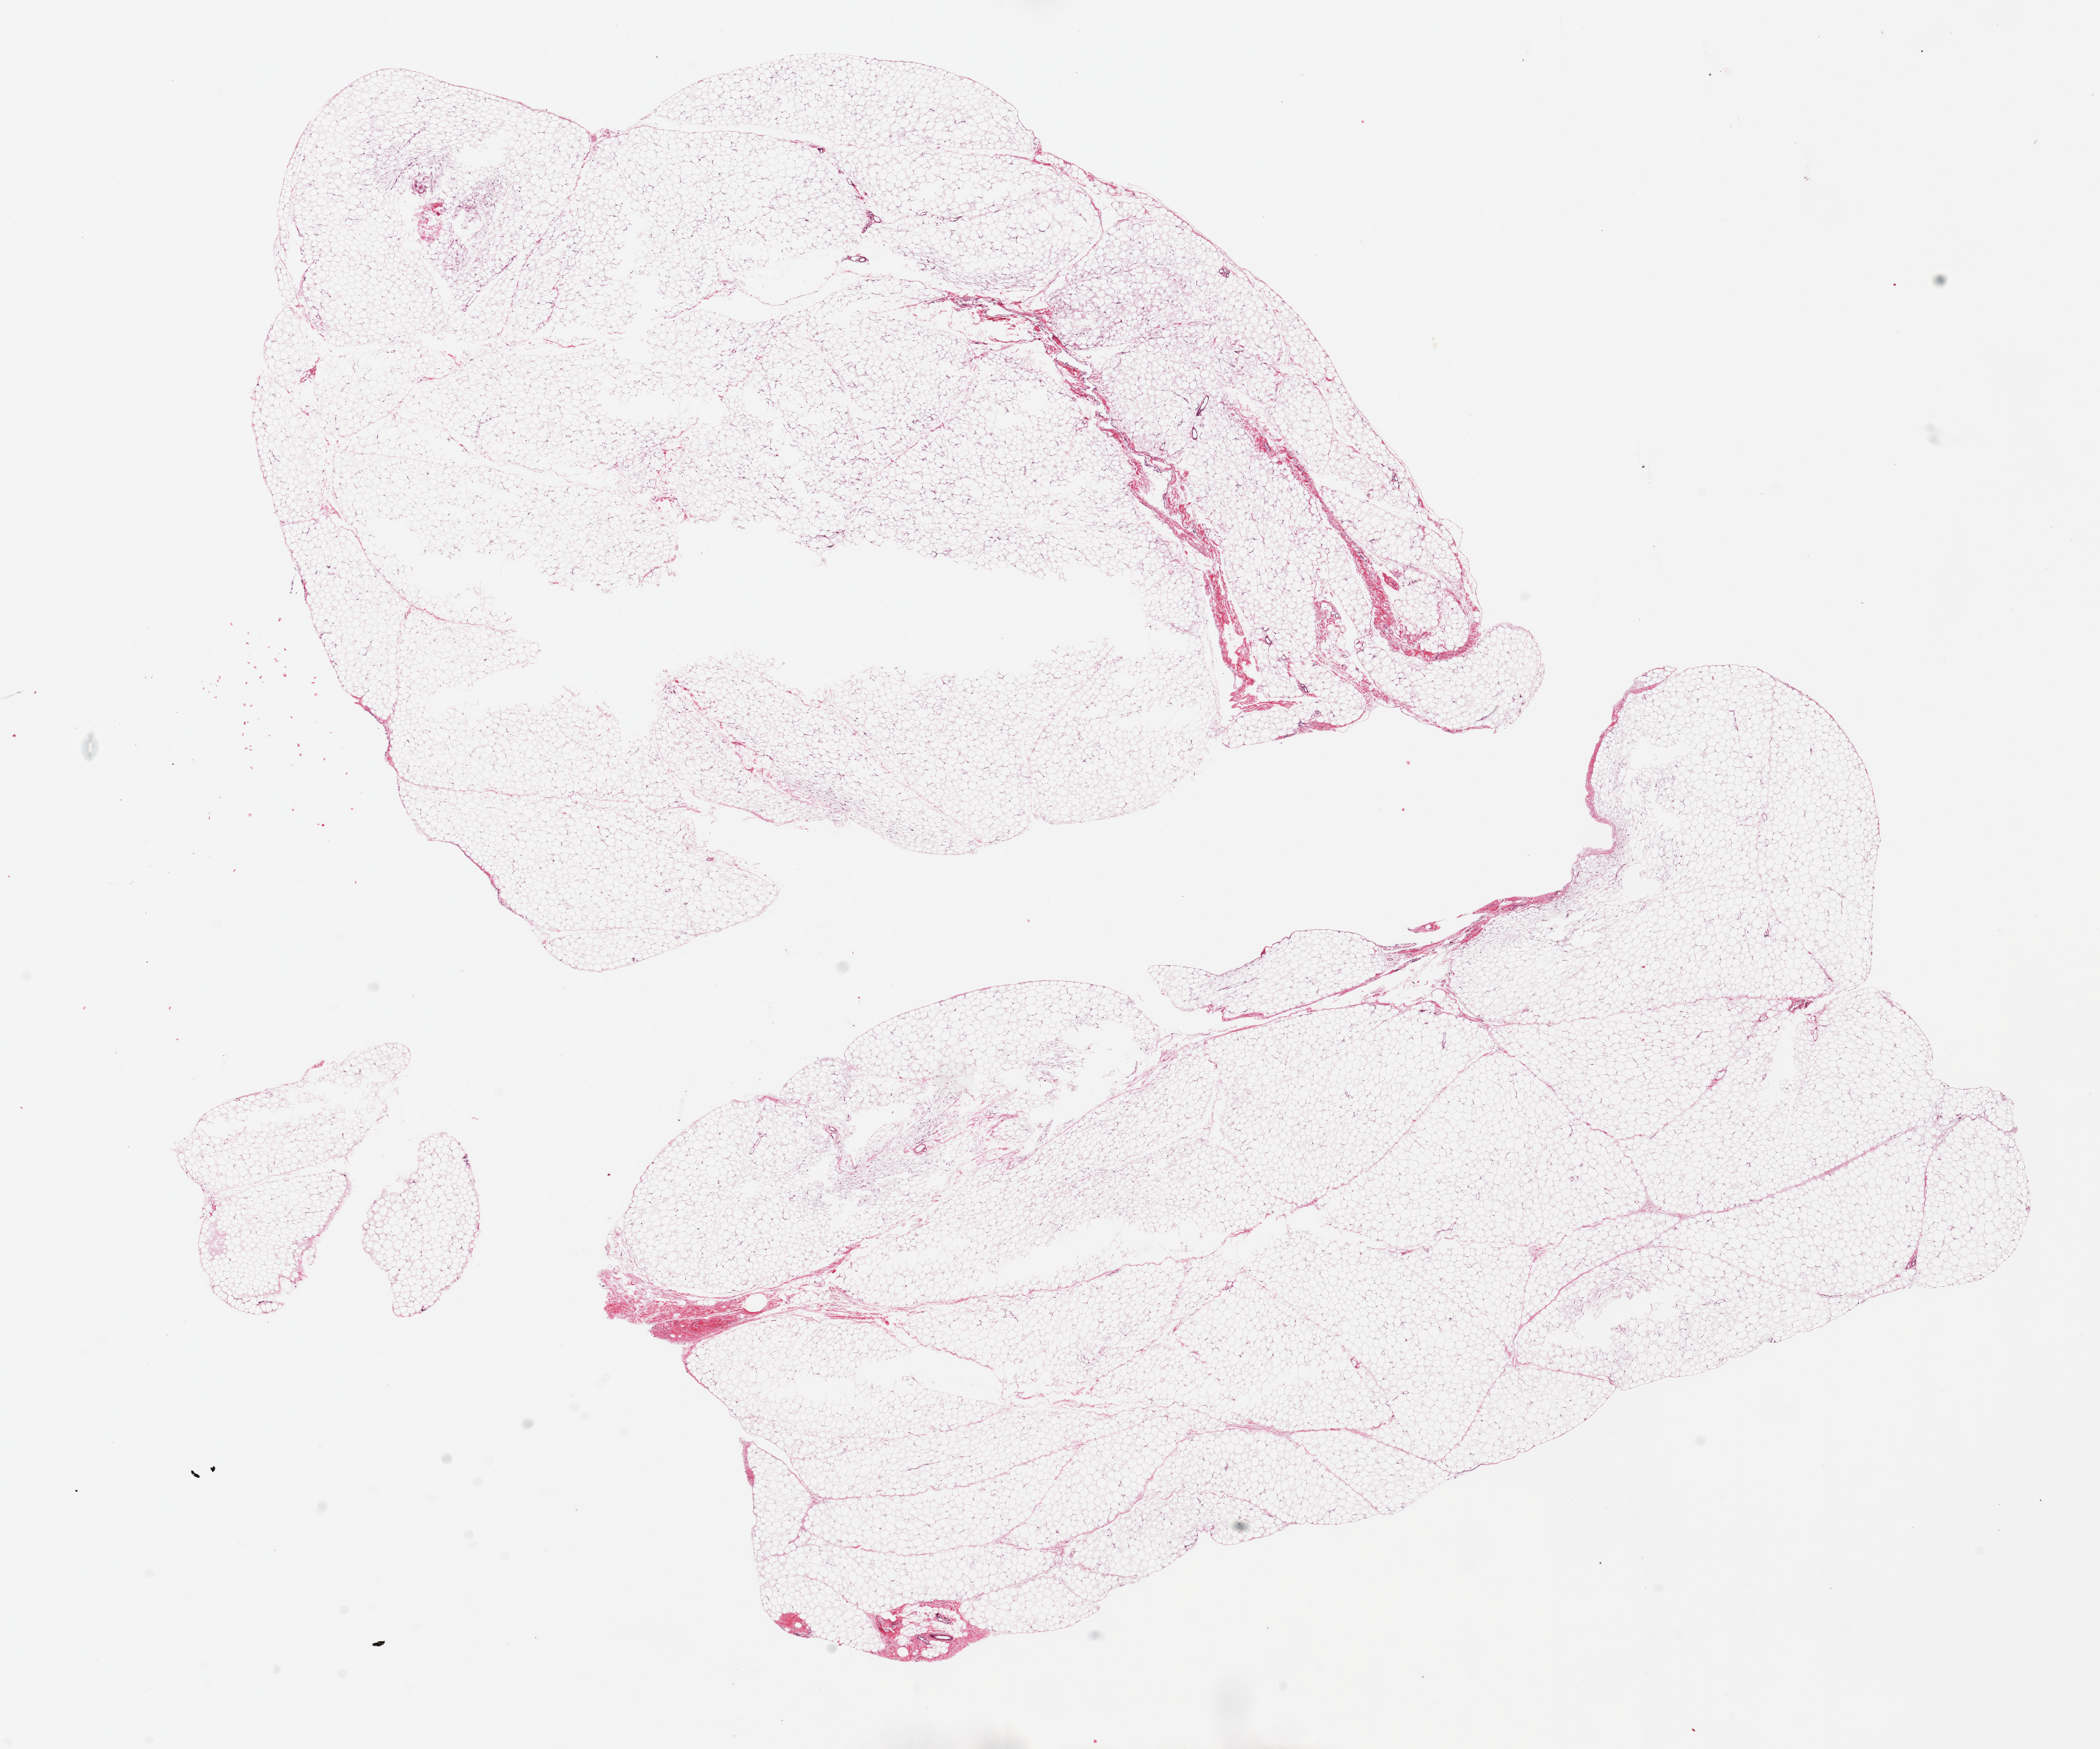
Hematoxylin and eosin (H&E) whole-slide image, brightfield — shown as a low-resolution overview of the whole scanned area (about 22.6 x 18.9 mm, slide scanned at 20x). PAXgene-fixed paraffin-embedded (PFPE) section. Section of omentum (target tissue). Donor tissue sample. Male donor.
* reviewer comment on this tissue sample: 2 pieces ~12x9mm